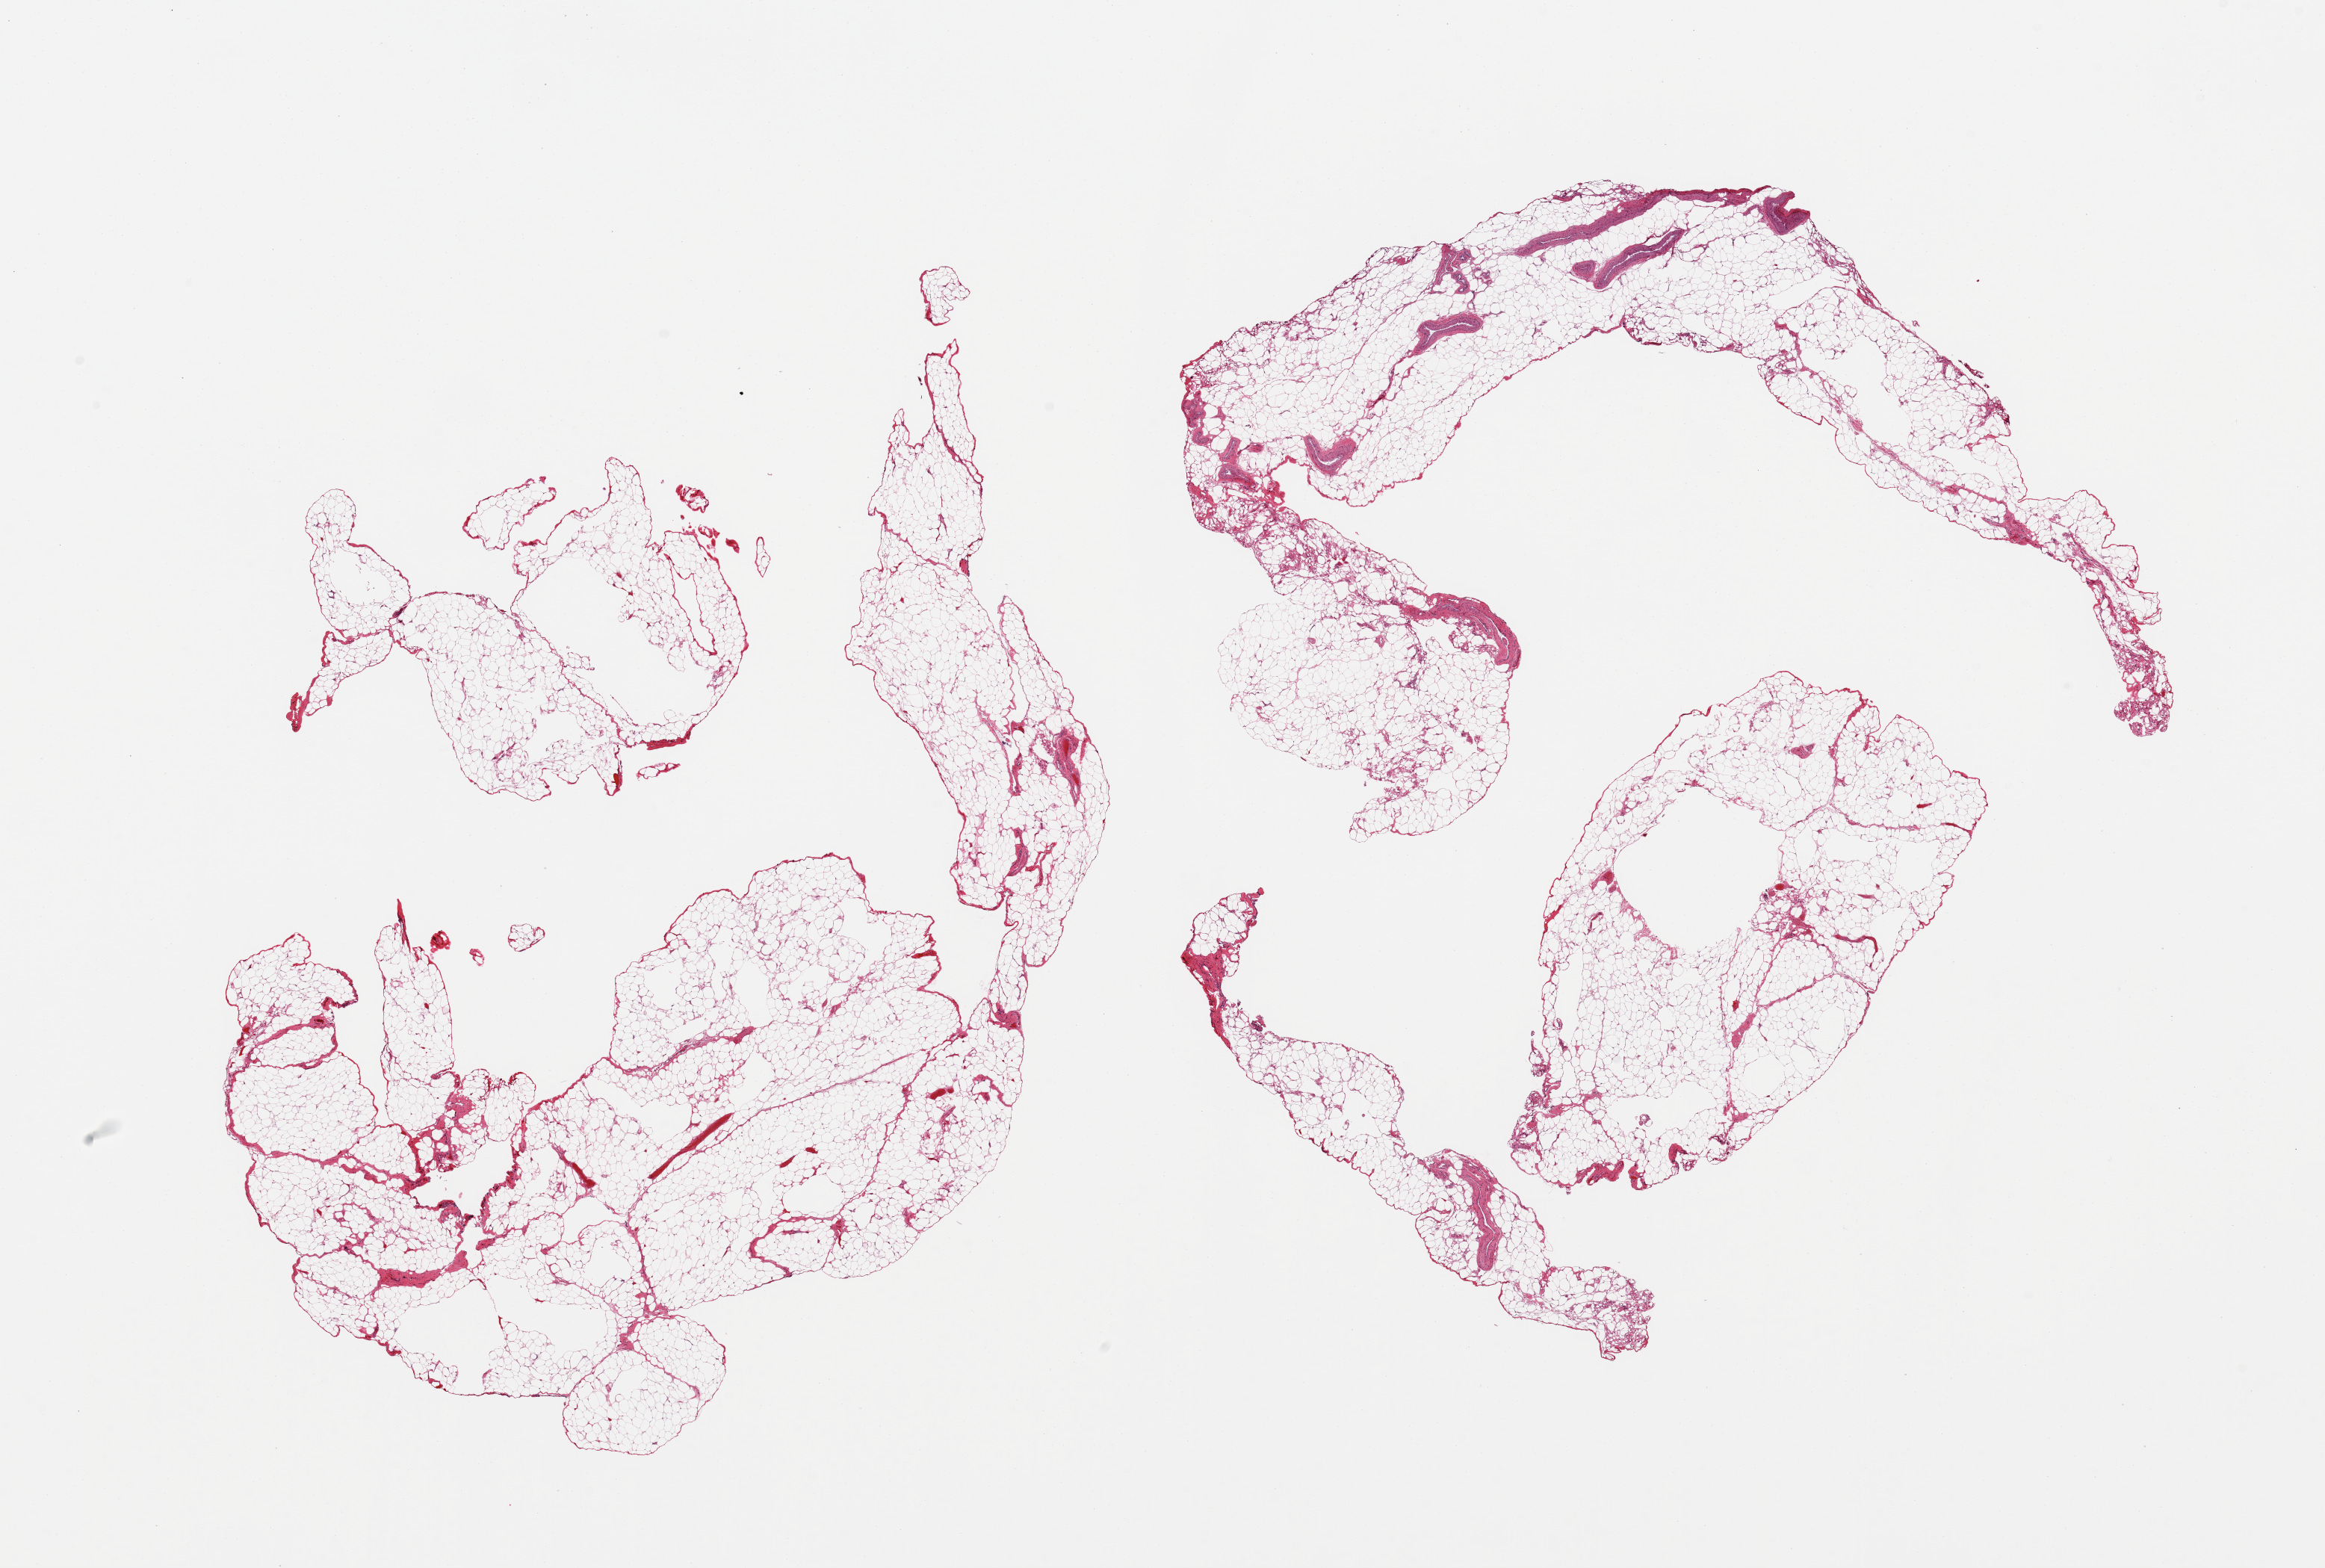
Digitized haematoxylin and eosin-stained section — shown as a low-resolution overview of the whole scanned area (about 24.6 x 16.6 mm); PAXgene-fixed, paraffin-embedded tissue; section of omentum (target tissue); donor tissue sample. Donor: male.
• pathologist's review note for this sample: 2 pieces, ~5-10% vascular elements/fascia